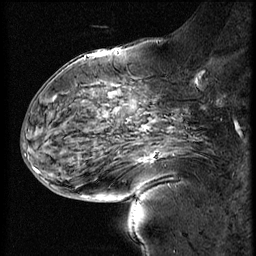
Breast MRI (dynamic contrast-enhanced), one sagittal slice; position 25 of 60 along the scan axis; 4 images stored at this slice position (order not interpretable as contrast timing); 1.5 T; TE 4.2 ms, TR 9 ms; 256 × 256 image matrix, field of view 180 × 180 mm. Female patient, age 56 years. Case-level facts recorded for this patient, not image findings: setting: breast cancer imaged before/during neoadjuvant chemotherapy; receptor status: HER2-positive.
Structures marked on this image (semi-automatically segmented with operator editing):
- analysis volume of interest (the breast-tissue region the enhancement analysis was run in; not a lesion): bounding box (x1, y1, x2, y2) in pixels: (110, 138, 192, 201)
- tumour enhancement mask (voxels above the 140 % enhancement threshold inside the analysis volume of interest): (147, 156, 153, 160)